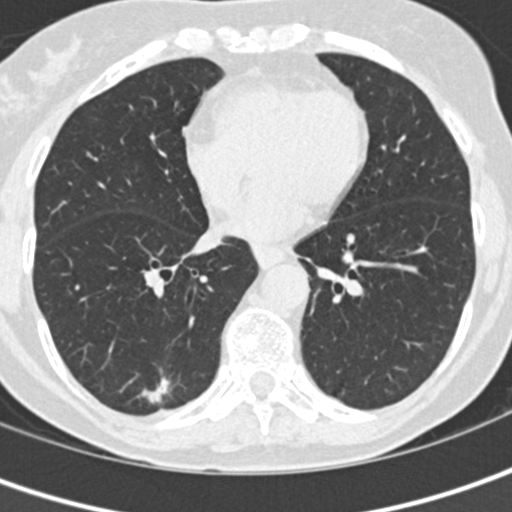
Low-dose screening chest CT, one axial slice; 120 kVp; lung window (W 1500 / L -600 HU); 512 × 512 image matrix.
Annotated regions visible in this slice (expert manual segmentation):
- lesion 1 (tumor, lower lobe of right lung): bounding box [x1, y1, x2, y2] px = [141, 377, 170, 403]